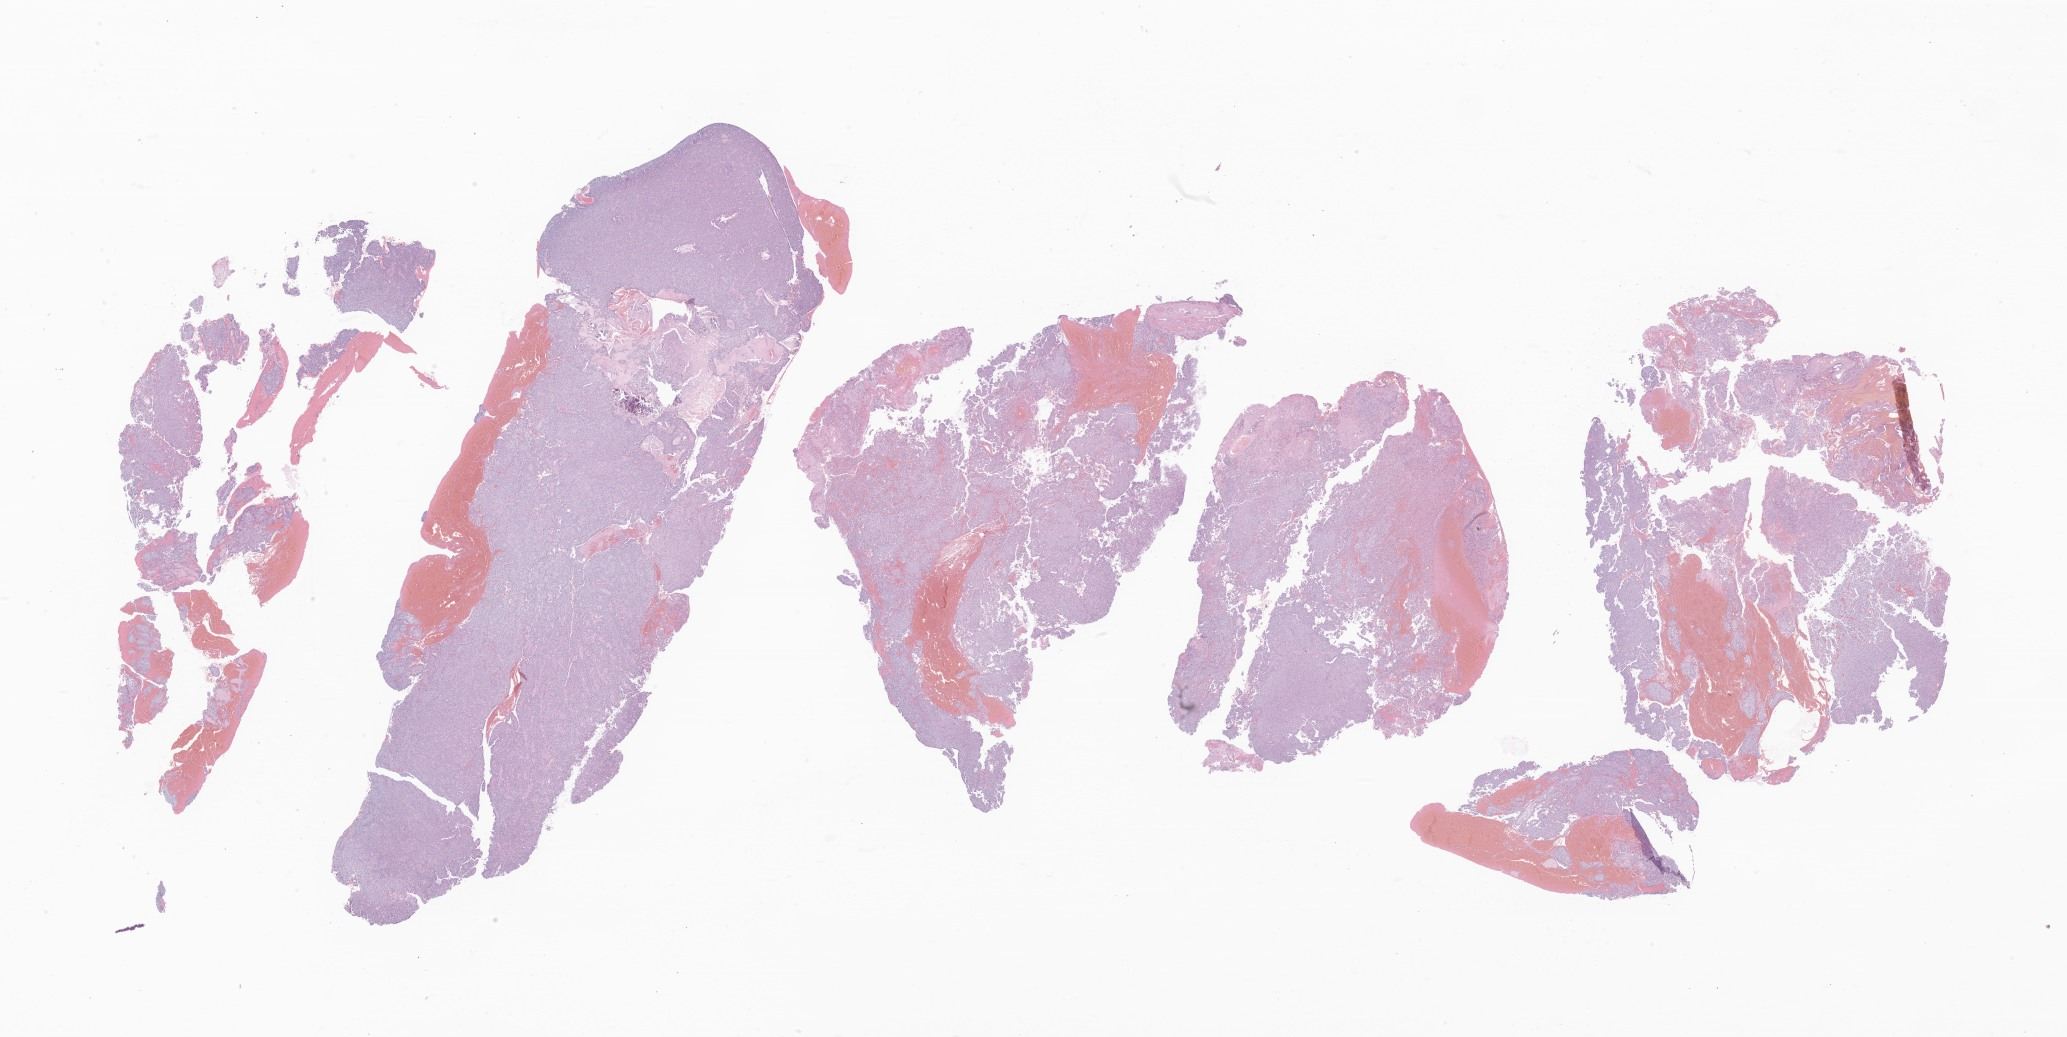
Whole-slide image, haematoxylin and eosin stain of tumor tissue from the brain — low-resolution overview of the scanned area, about 34.9 x 17.5 mm. FFPE section. Female patient, age 64 months (5 years 4 months).
* recorded diagnosis: Oligoastrocytoma, NOS